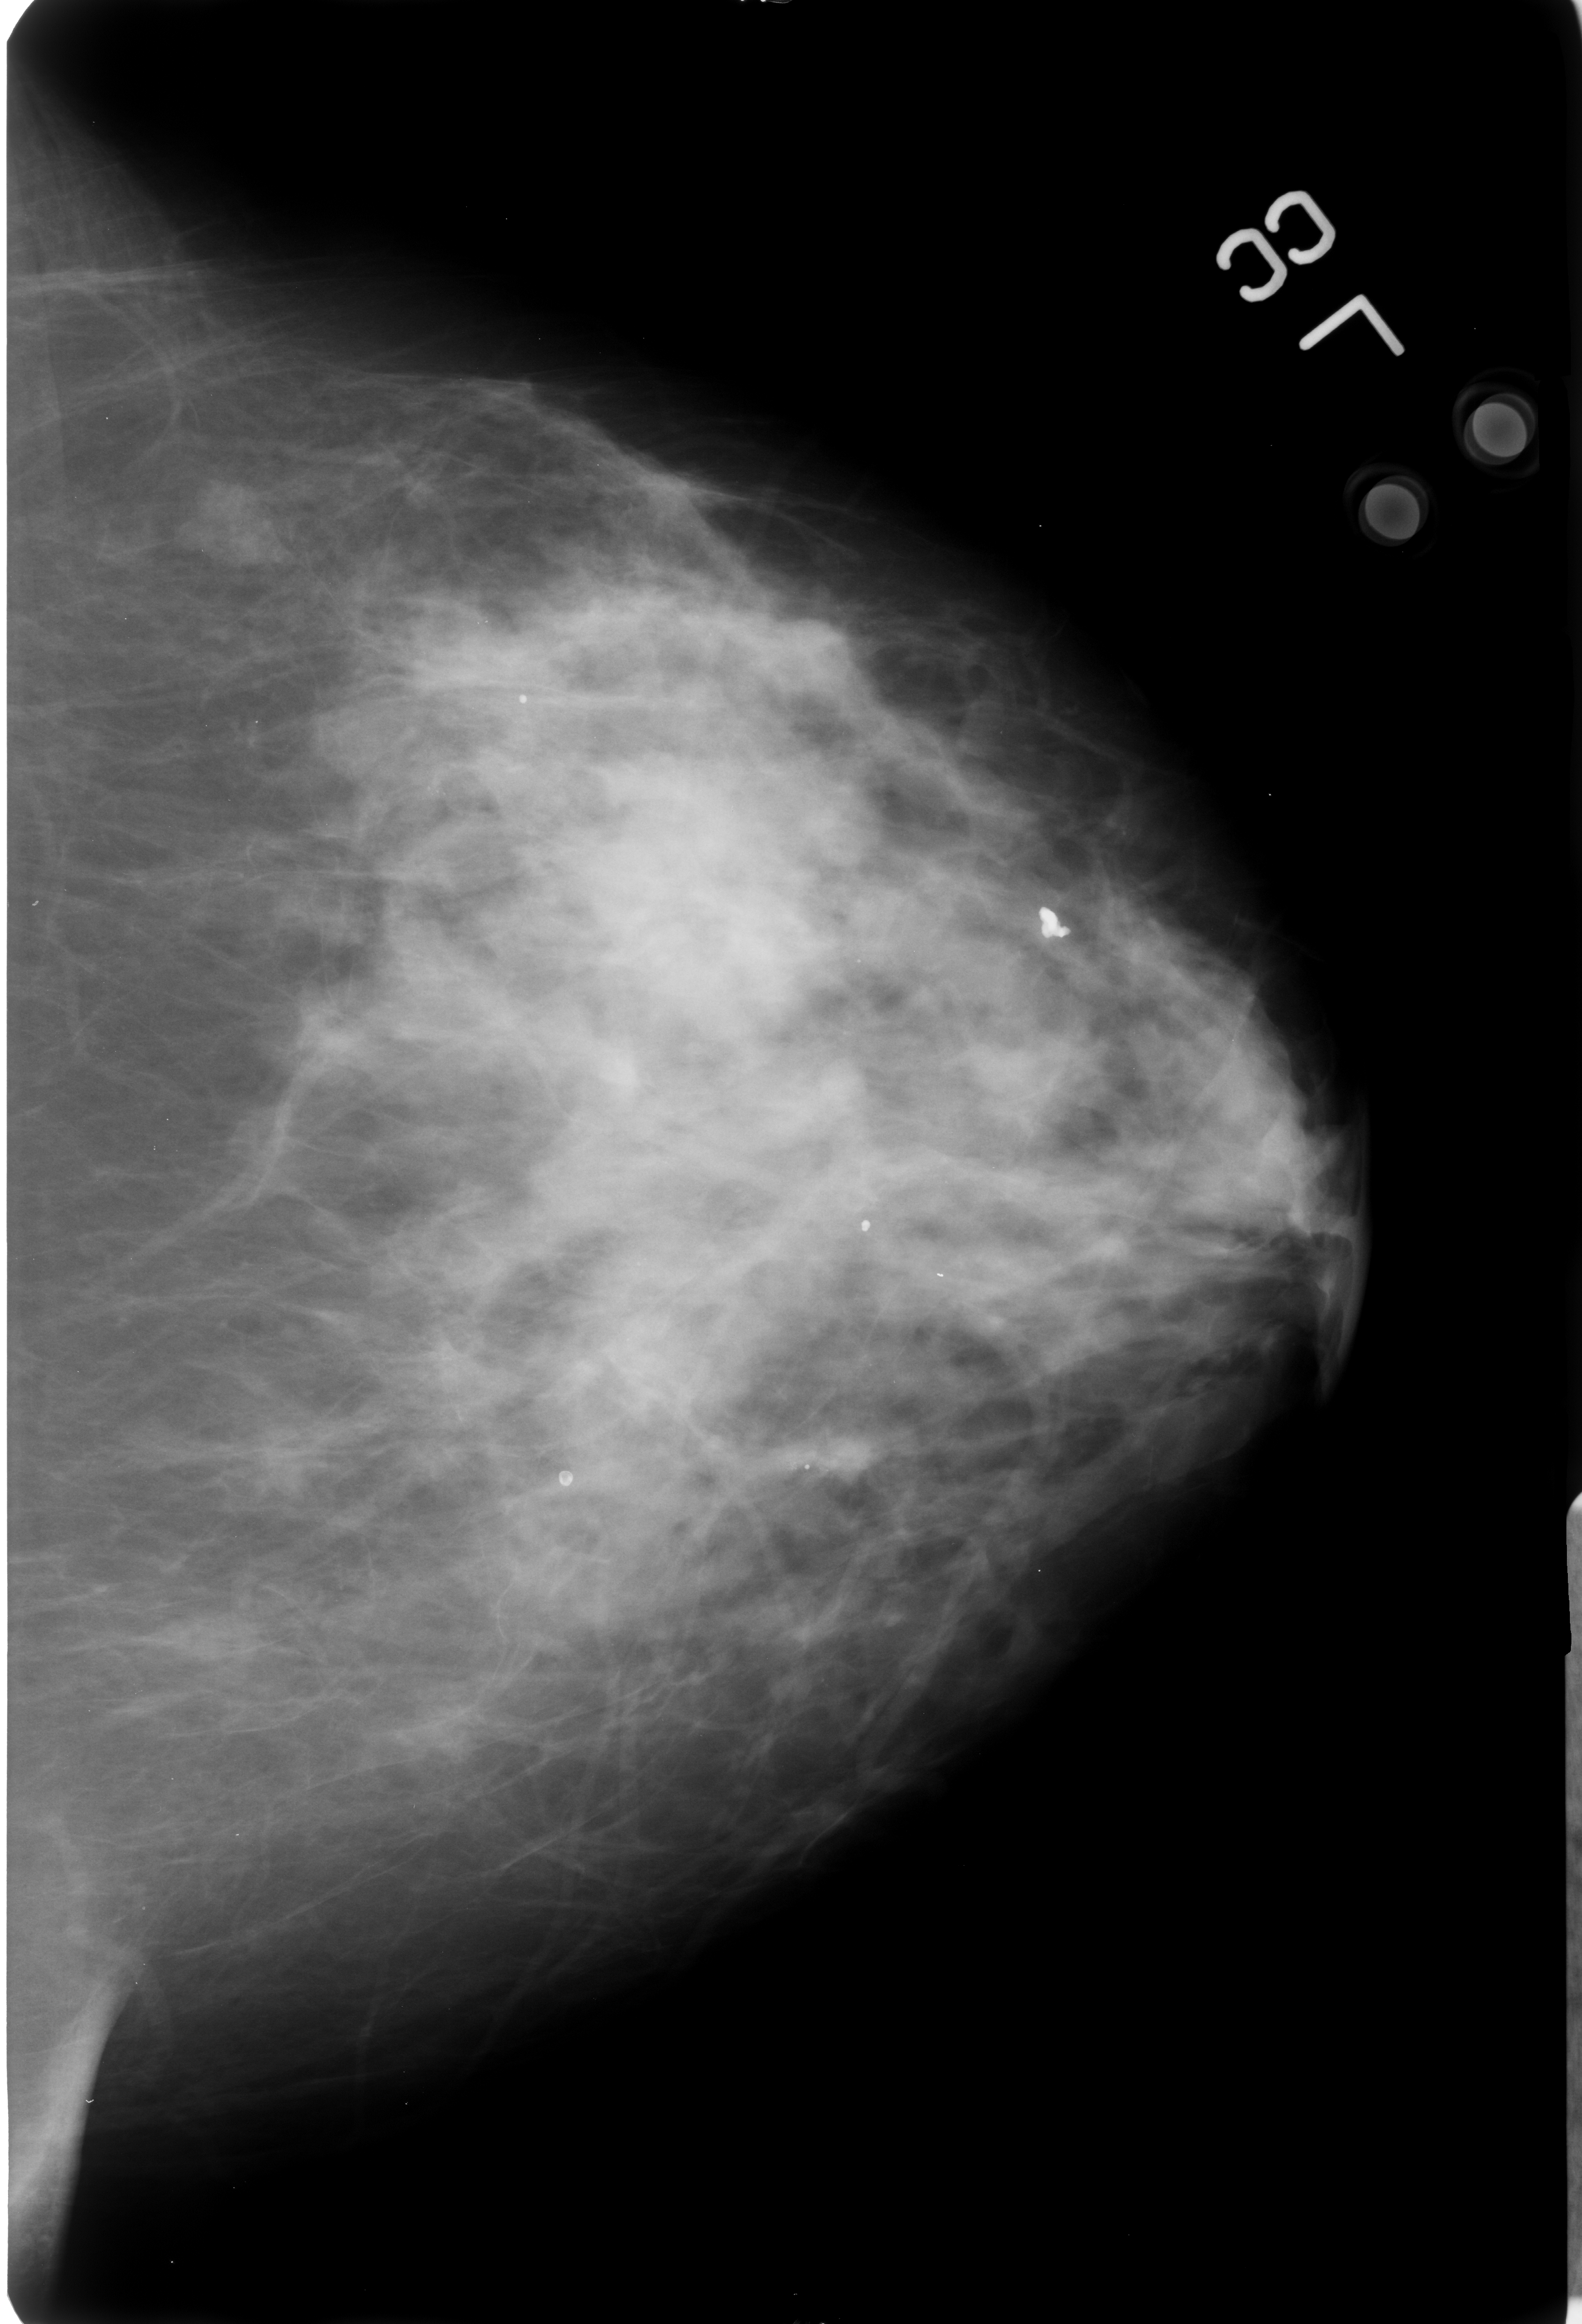
Scanned film-screen mammogram, left breast, craniocaudal (CC) view, breast composition: heterogeneously dense (BI-RADS density category 3 of 4).
- Marked findings (only marked abnormalities are described; nothing is implied about the rest of the image): calcifications, morphology round and regular / lucent center / dystrophic, distribution diffusely scattered; BI-RADS assessment category 2; subtlety rating 4 on a 1 (subtle) to 5 (obvious) scale; benign without callback (not worked up further).